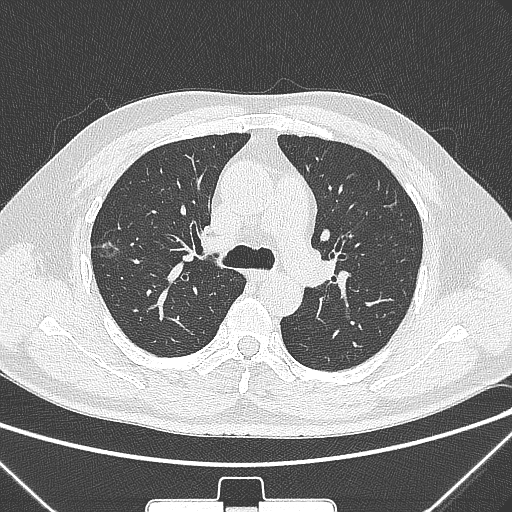
Chest CT, one axial slice. Position 203 of 320 along the scan axis. 120 kVp. Lung window (W 1500 / L -600 HU). 512 × 512 image matrix. Male patient, age 58 years. From the clinical record (not read from this slice): clinical TNM (as recorded): T1c N0 M0.
Annotated regions visible in this slice (bounding box drawn by a radiologist):
- lung tumour (recorded histology: adenocarcinoma): bounding box (x1, y1, x2, y2) in pixels: (95, 230, 131, 268)